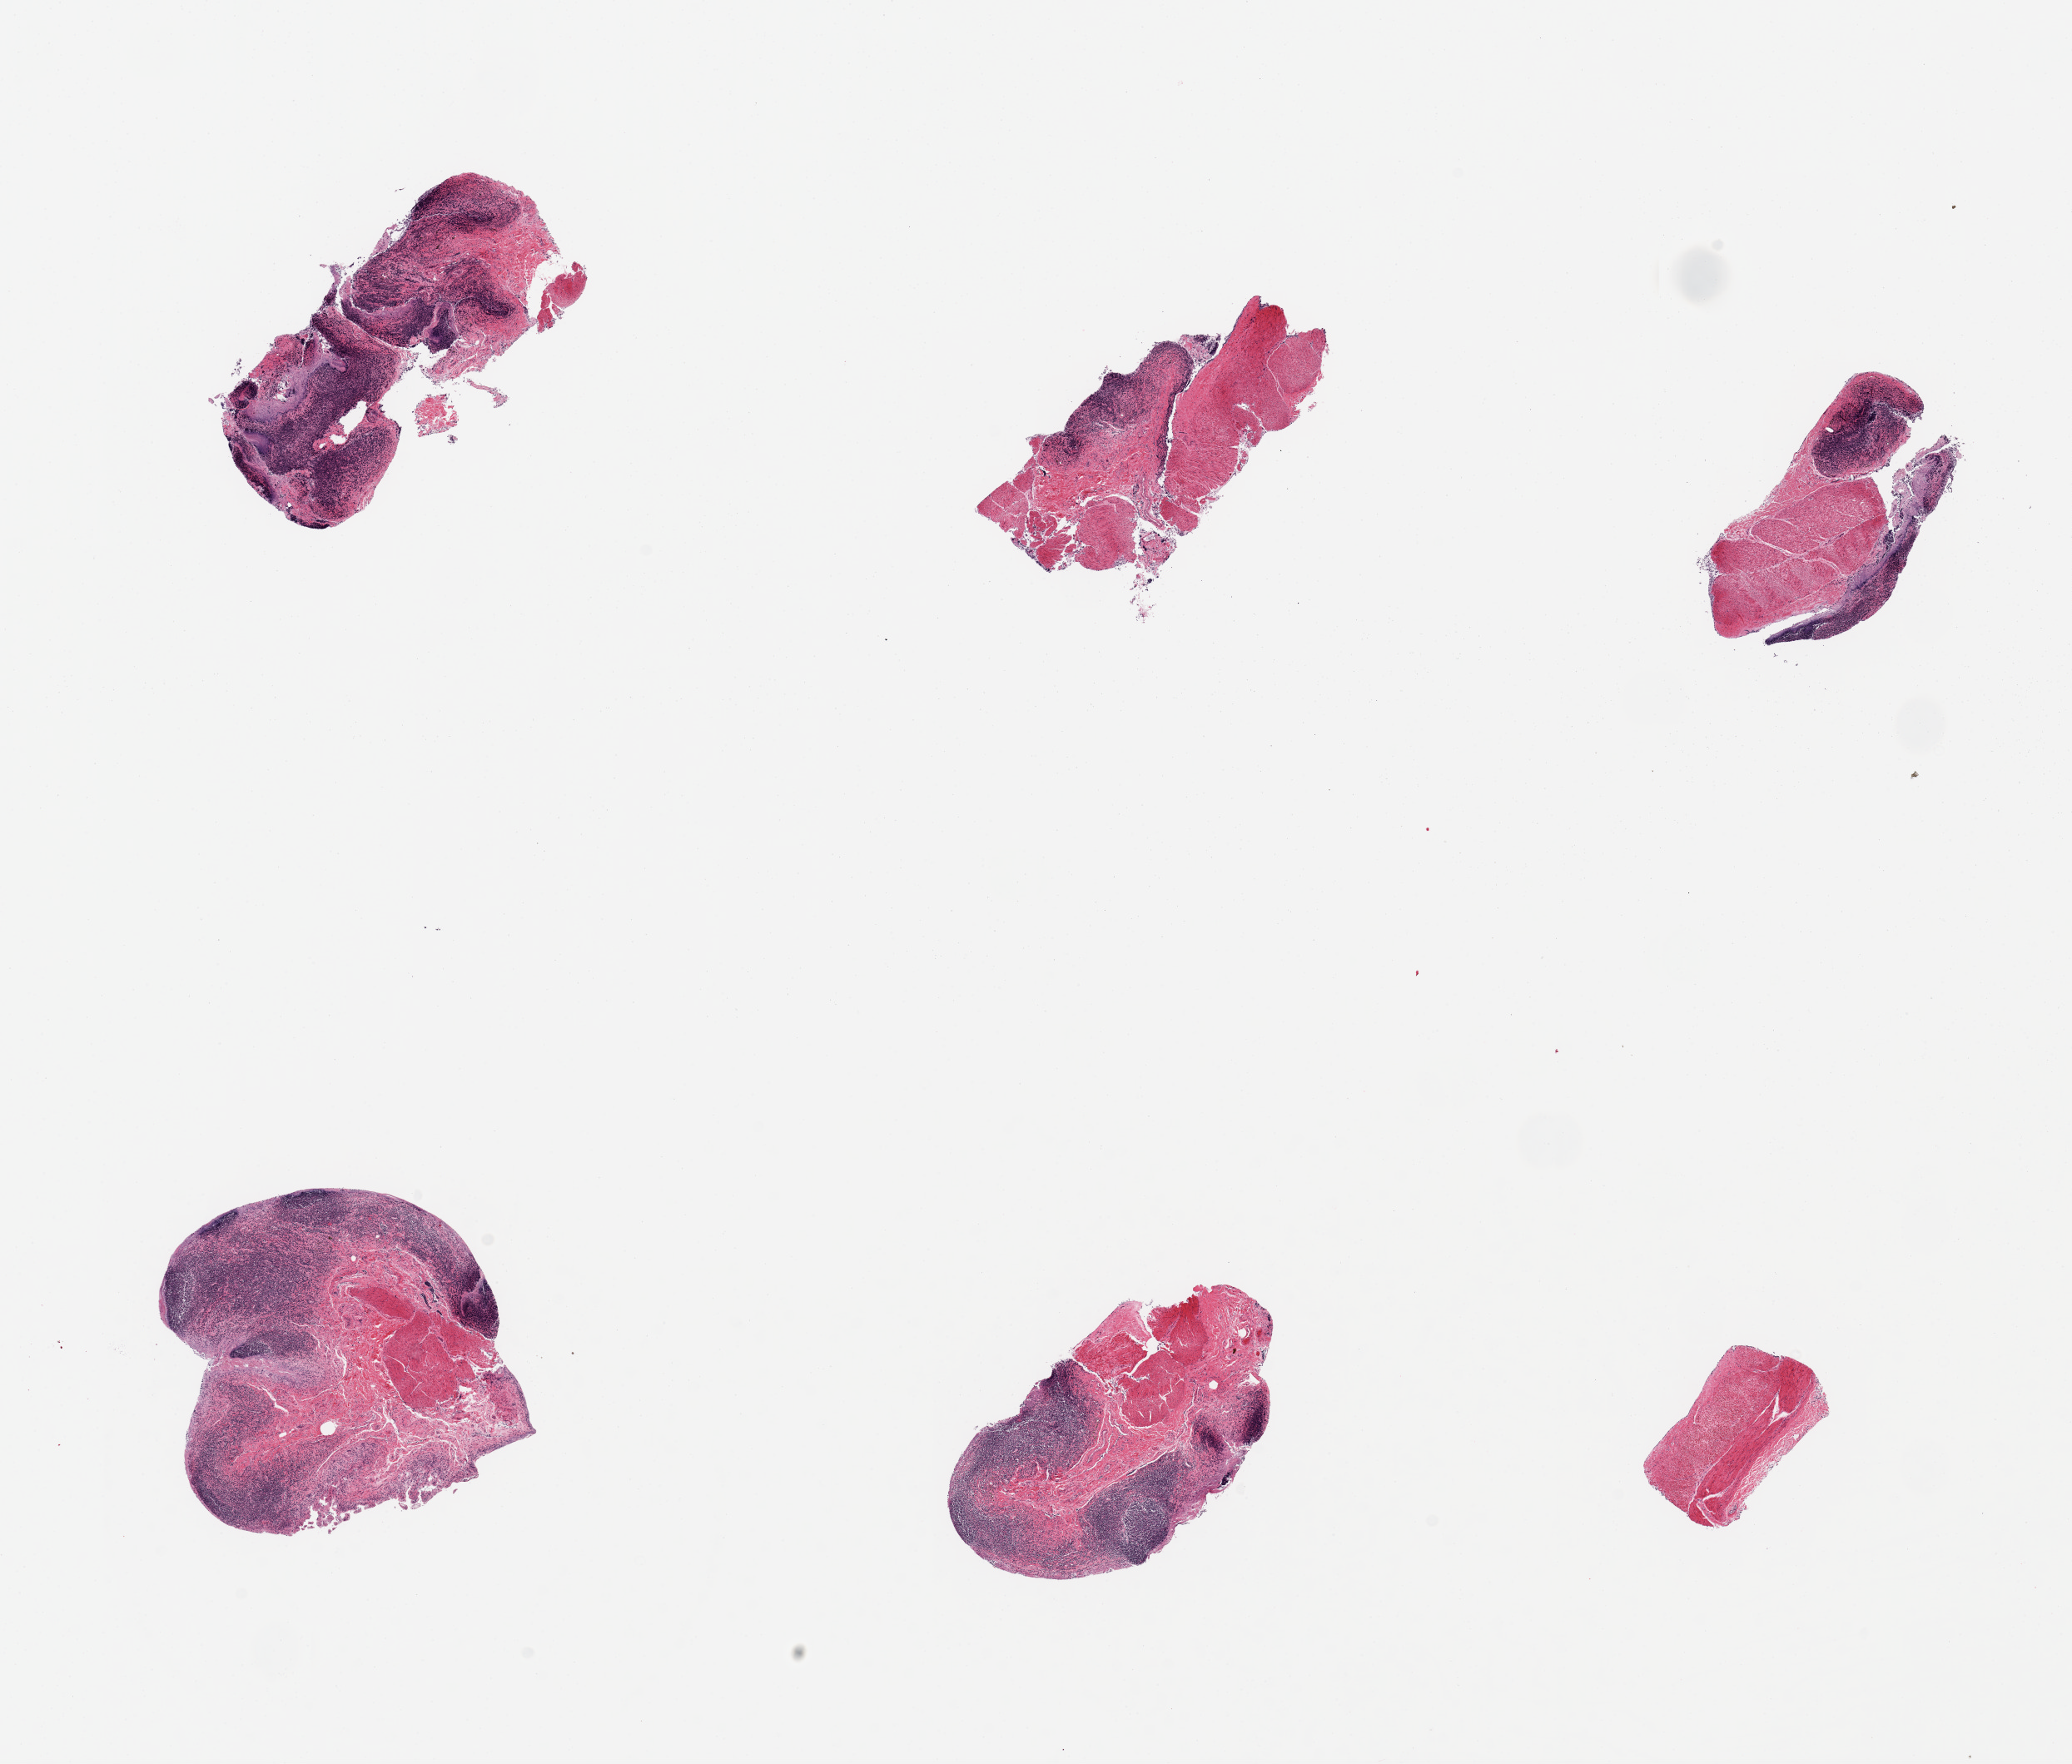
Haematoxylin and eosin whole-slide image — whole scanned area (about 19.7 x 16.8 mm, from a 20x scan) shown as a low-resolution overview. PAXgene-fixed, paraffin-embedded tissue. Section of ileum (target tissue). Tissue donor sample. Donor sex: female.
Reviewer comment on this tissue sample: 6 pieces, good lymphoid component, but includes abundant muscularis.